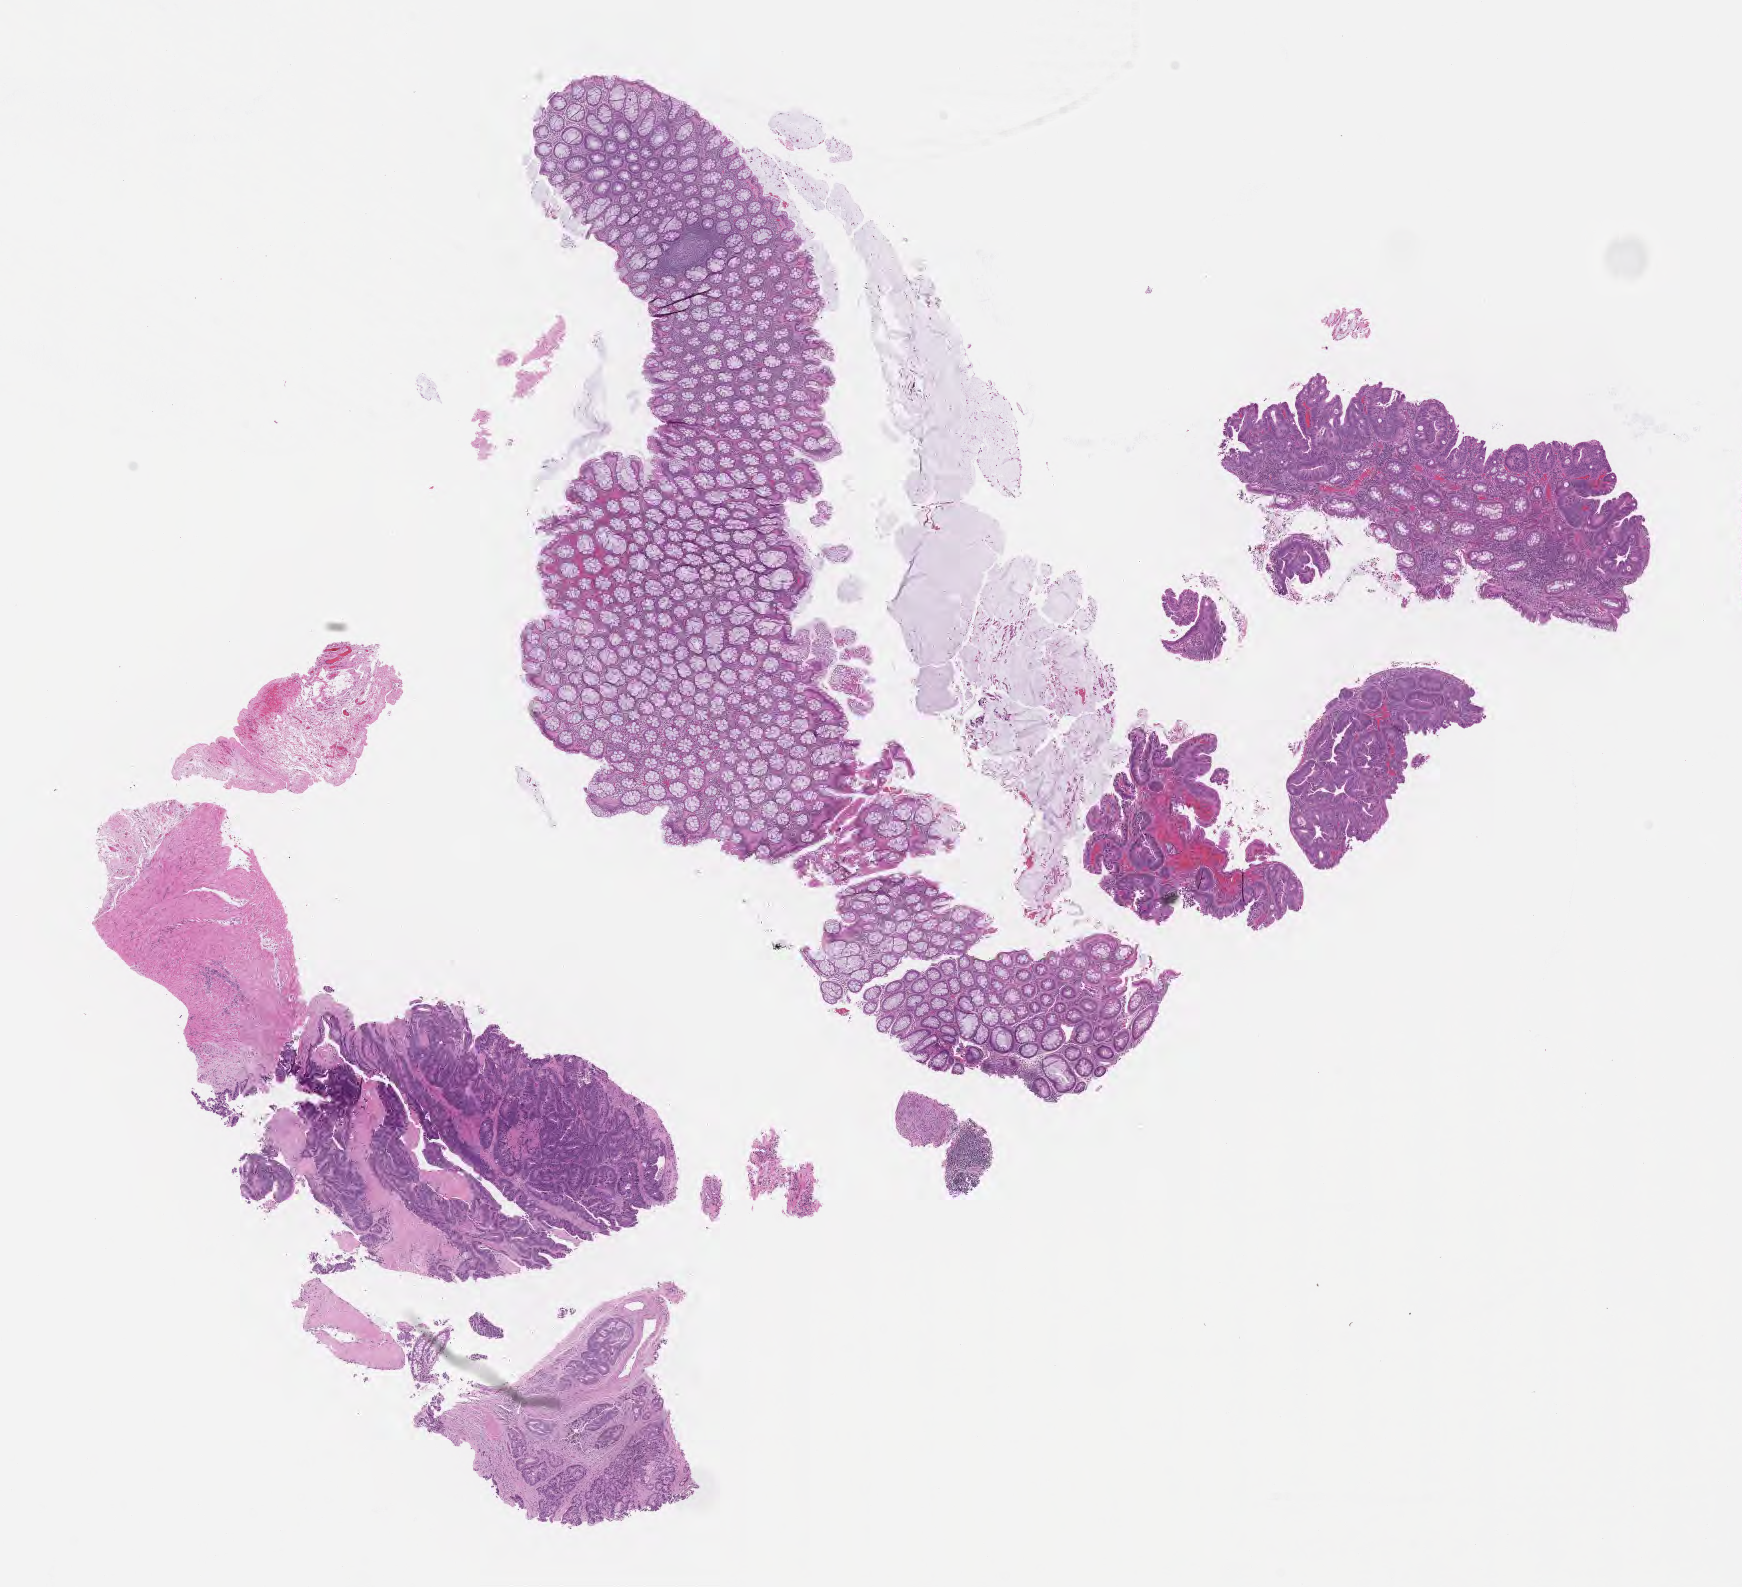
Whole-slide image, haematoxylin and eosin stain, shown as a low-resolution overview of the whole scanned area (about 14.1 x 12.8 mm); formalin-fixed, paraffin-embedded (FFPE) tissue; primary tumor; site: sigmoid colon. Male patient; age at initial diagnosis 72 years. Tumor grade: G2 (moderately differentiated). Pathologist review of this section (percent, as recorded): tumor cells 45%, tumor nuclei 50%, stromal cells 0%, necrosis 0%, normal cells 55%. Inflammatory infiltration, as recorded: lymphocyte infiltration 0%, monocyte infiltration 0%, neutrophil infiltration 0%.
AJCC pathologic stage: Stage IIA. Section: top of the tissue portion. Histologic diagnosis: Adenocarcinoma, NOS.